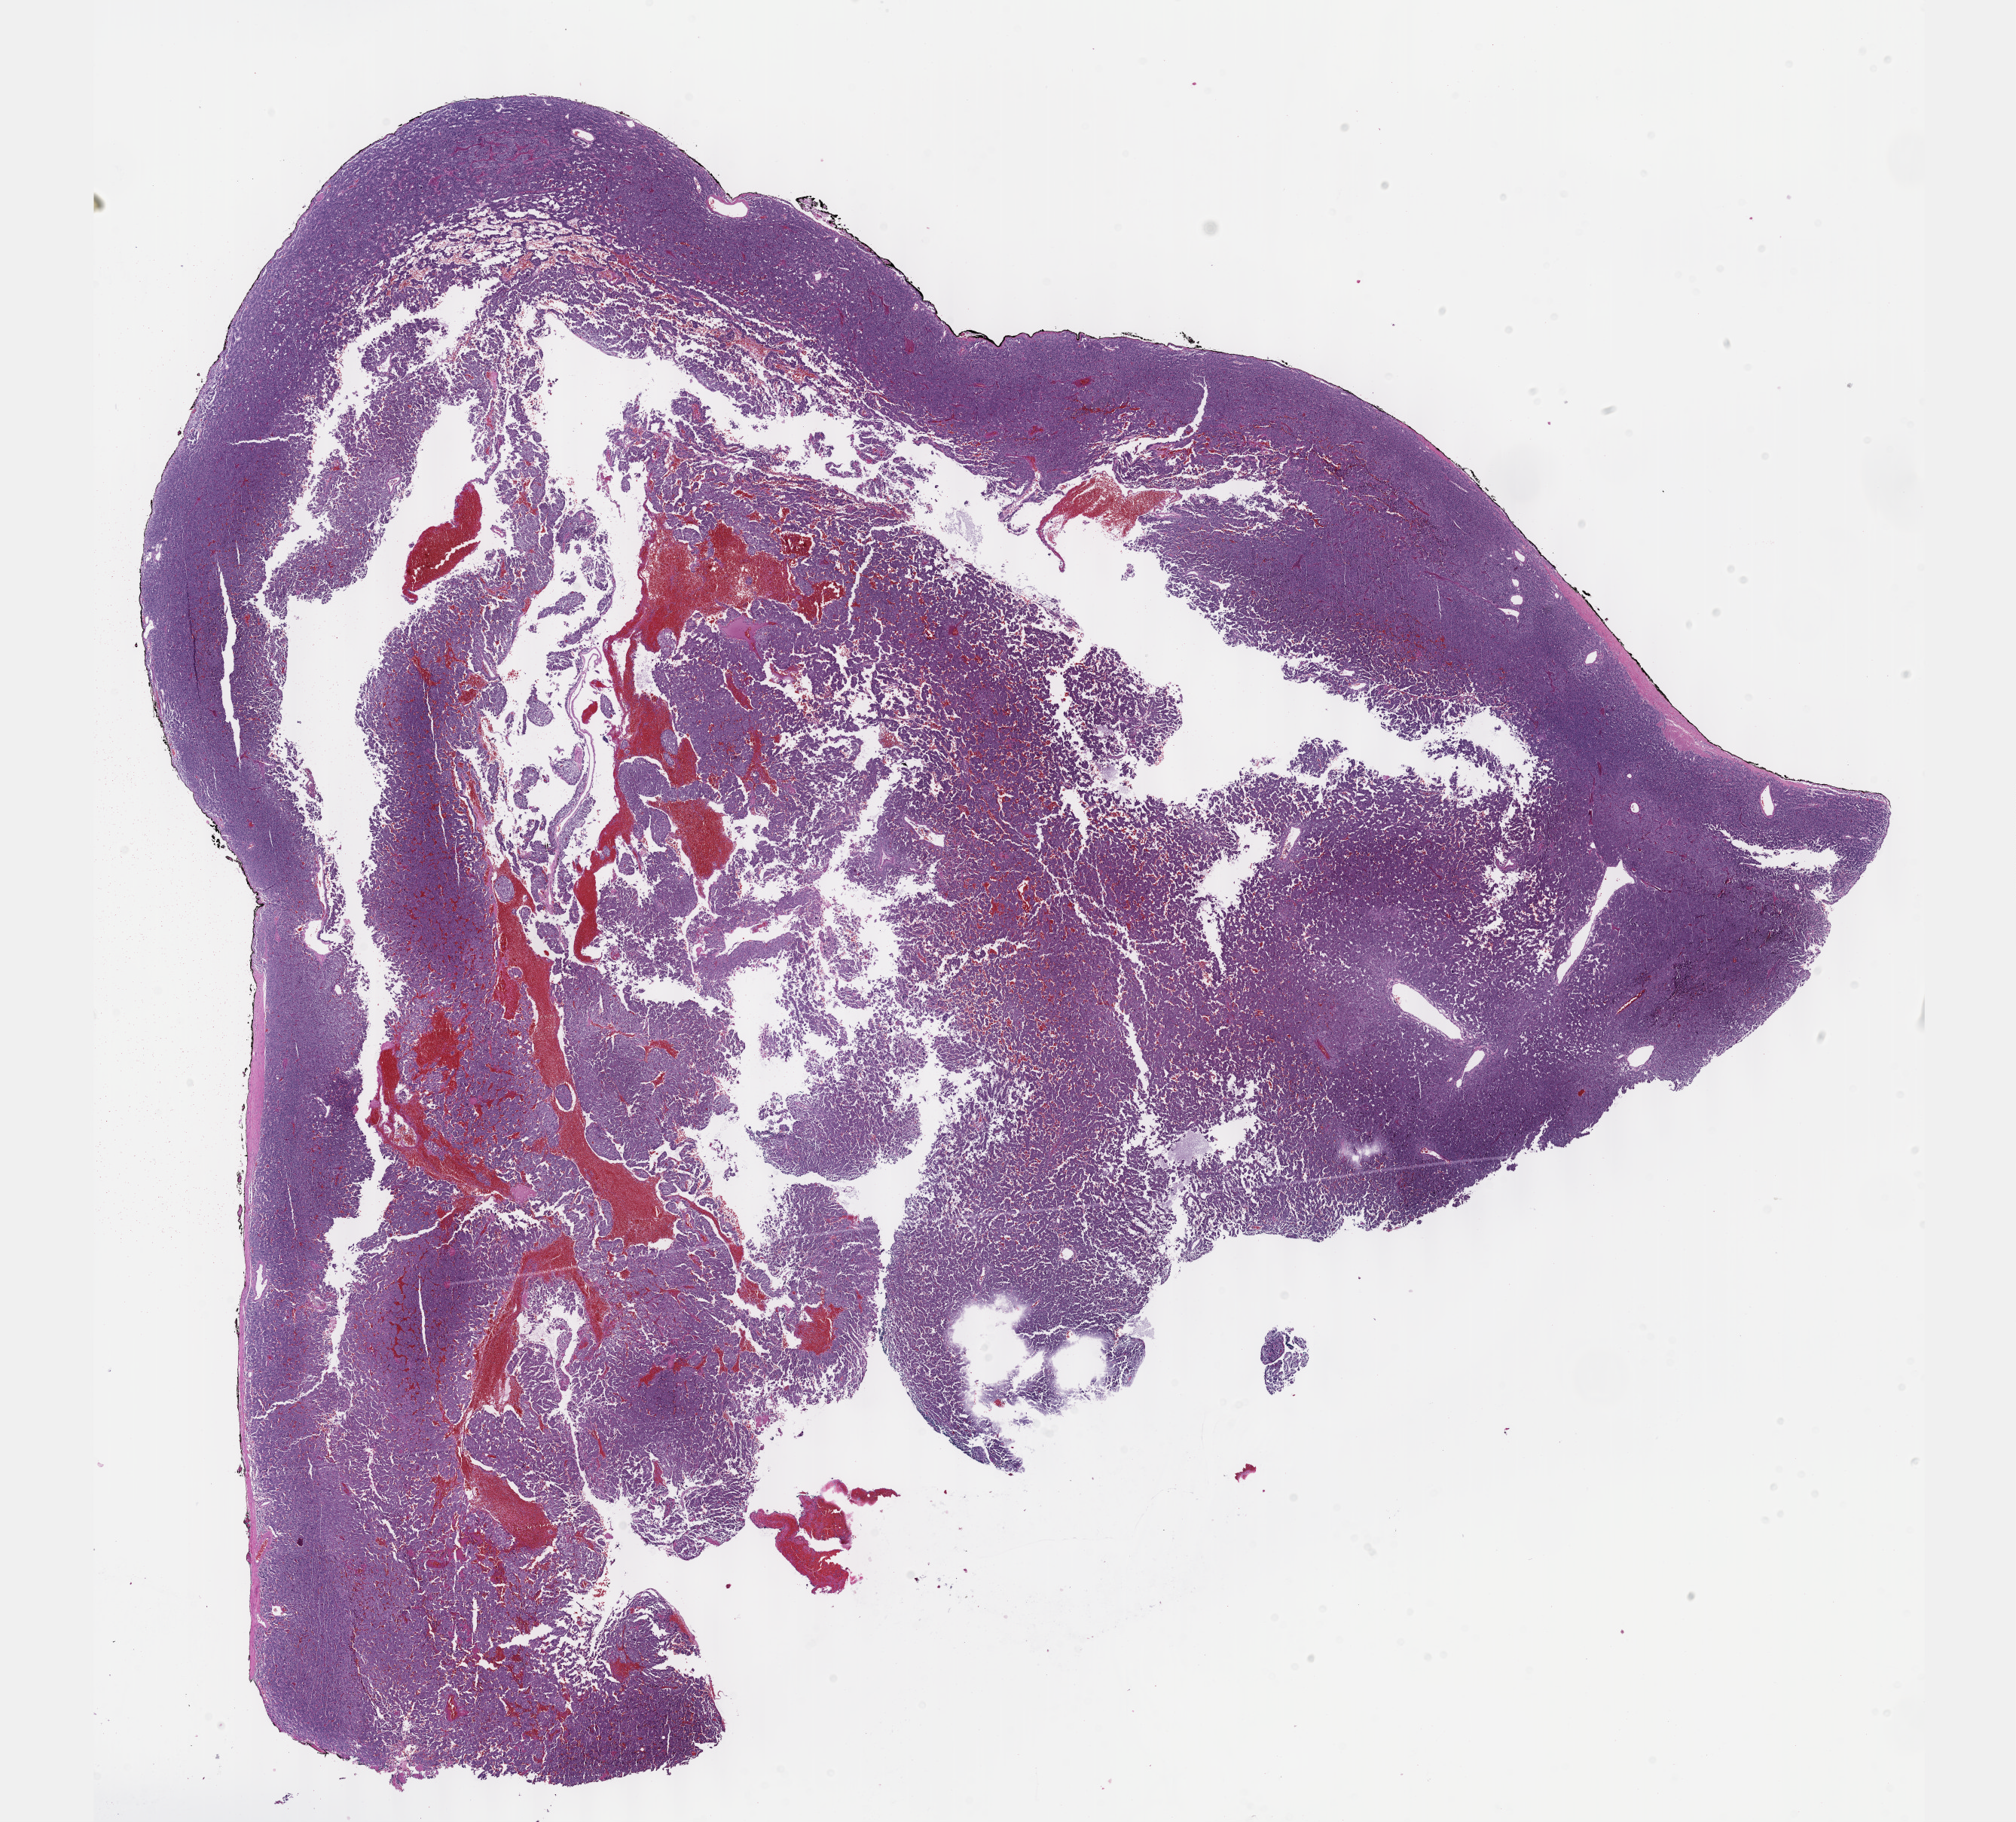
Whole-slide histology image, H&E-stained — shown as a low-resolution overview of the whole scanned area (about 21.6 x 19.6 mm, slide scanned at 40x). FFPE section. Primary tumour sample from the retroperitoneum and peritoneum. Female patient; age at initial diagnosis 75 years.
• histologic diagnosis: Extra-adrenal paraganglioma, NOS
• lymph nodes positive (case pathology): 0 of 4 examined